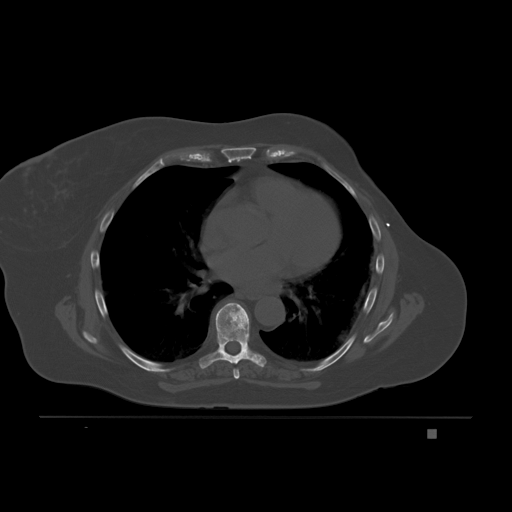
CT including the spine, one axial slice; position 128 of 221 along the scan axis; bone window (W 1800 / L 400 HU); 3 mm slice thickness; 512 × 512 image matrix. Female patient, age 63 years. Case-level facts recorded for this patient, not image findings: primary cancer: breast.
Outlined on this slice (semi-automatically segmented with operator editing):
- T6 vertebra: bounding box [x1, y1, x2, y2] px = [233, 368, 240, 379]
- T7 vertebra: [199, 302, 267, 369]